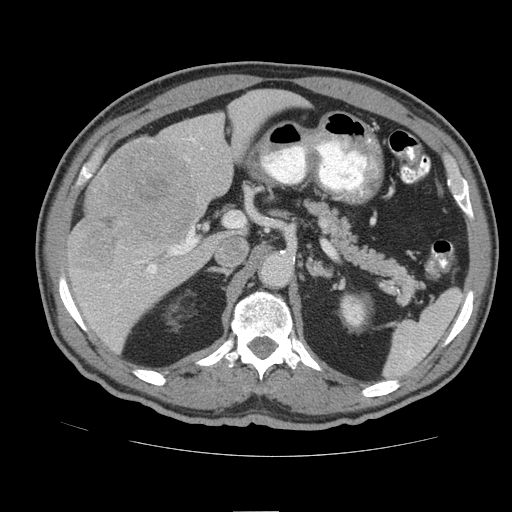
Contrast-enhanced abdominal CT (liver protocol), one axial slice; position 52 of 105 along the scan axis; 140 kVp; soft-tissue window (W 400 / L 40 HU); 512 × 512 image matrix, field of view 380 × 380 mm. Case-level facts recorded for this patient, not image findings: diagnosis: hepatocellular carcinoma (patient treated with transarterial chemoembolisation; whether this scan precedes or follows treatment is not stated here); TNM stage (as recorded): Stage-IIIB; Child-Pugh class: A; tumour nodularity: multinodular.
Annotated regions visible in this slice (semi-automatically segmented with operator editing):
- liver parenchyma outside the tumour (the mass and vessels are separate outlines, so this box may not span the whole liver): box from (x=66, y=88) to (x=304, y=353) px
- mass: (x=72, y=141)–(x=199, y=269)
- liver vessels: (x=129, y=137)–(x=195, y=275)